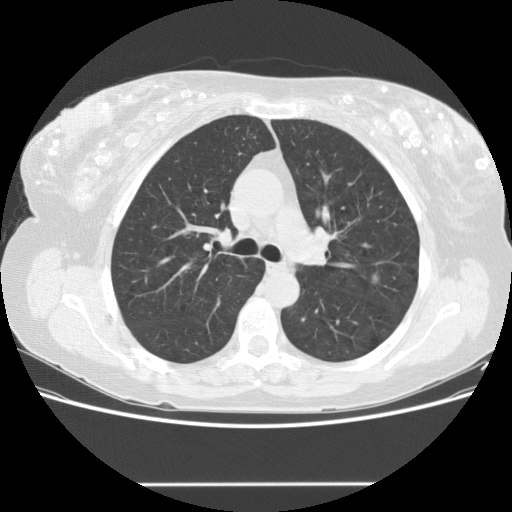
Low-dose screening chest CT, axial slice, second screening round (one year after baseline), lung window (W 1500 / L -600 HU), 2.5 mm slice thickness, standard (soft-tissue) reconstruction kernel (STANDARD). Female, age 57 years at enrolment. Current smoker at enrolment.
Lesion marked by an expert reader, box from (x=357, y=262) to (x=393, y=296) px. Screening reader's record for this exam (one nodule recorded; not confirmed to be the boxed lesion): non-calcified nodule or mass ≥4 mm, lingula, 10 × 8 mm, smooth margins, soft tissue attenuation, pre-existing on the prior screen: no. Official screen result: positive, other. Lung cancer was diagnosed 125 days after this screen: large cell neuroendocrine carcinoma, left upper lobe, poorly differentiated (G3), stage IB (AJCC 6th edition), 10 mm at pathology.